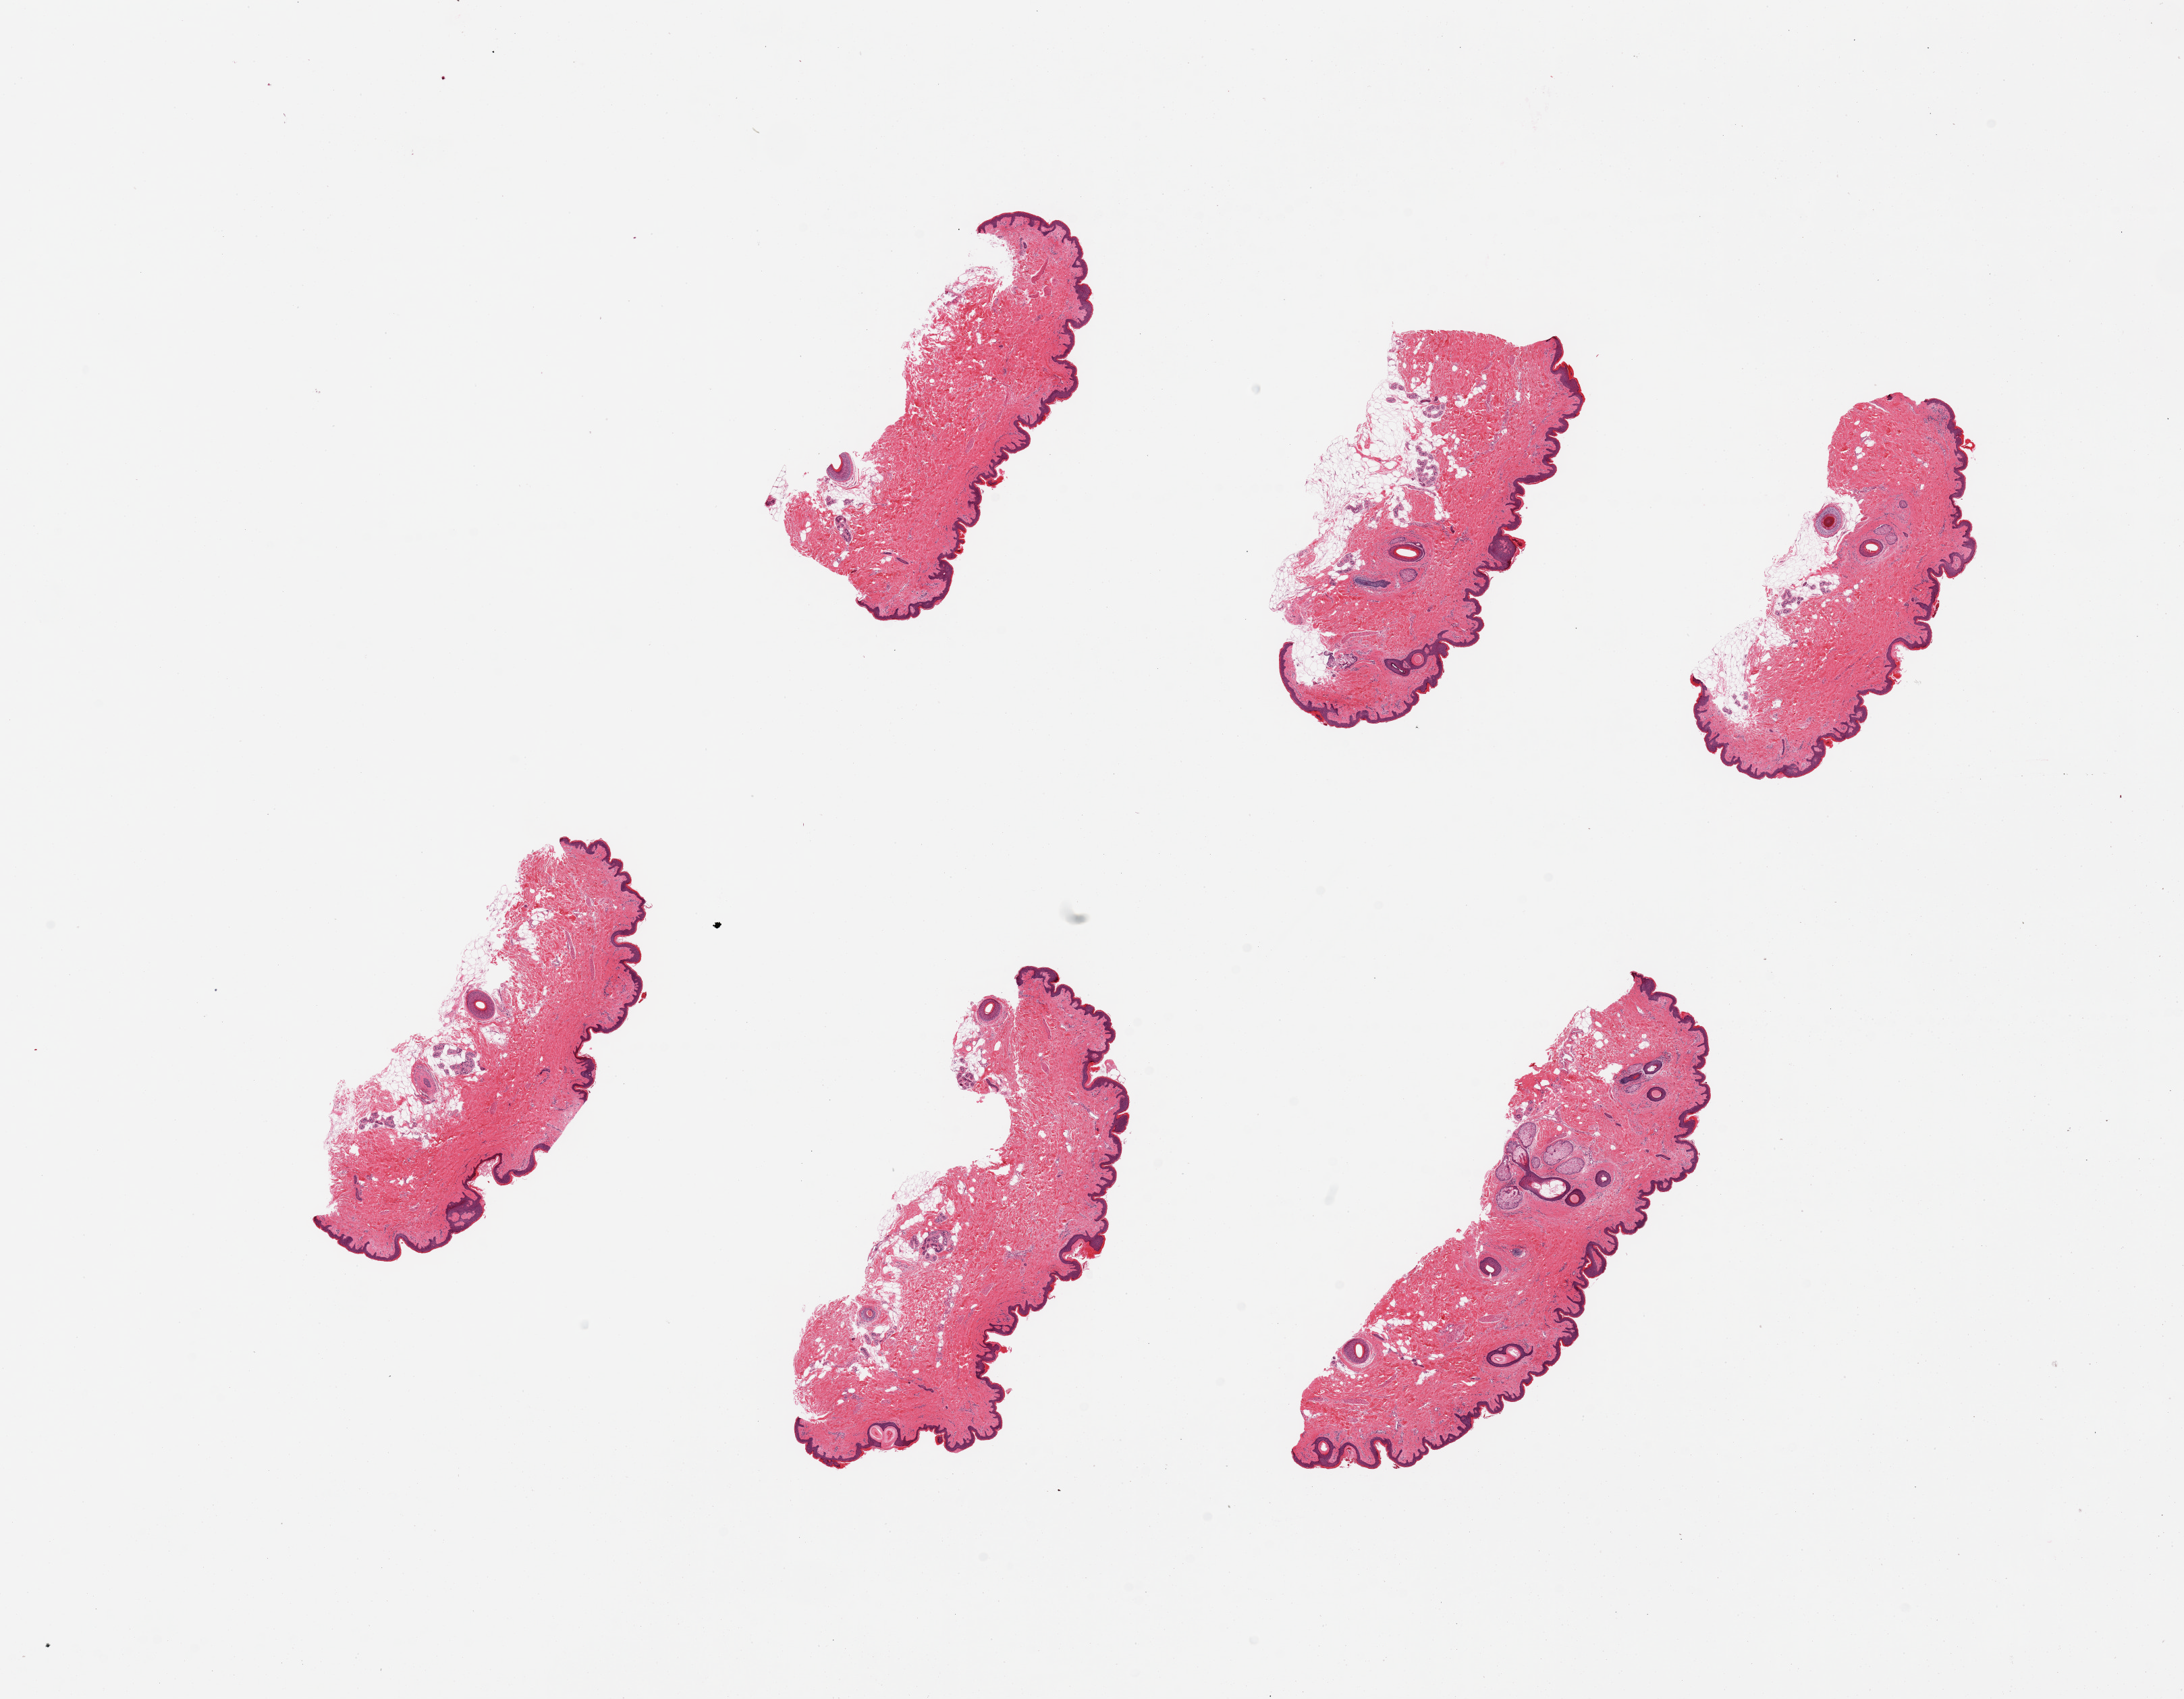
Whole-slide image, hematoxylin and eosin (H&E) stain, brightfield — a low-resolution overview of the entire scanned area, about 25.6 x 19.9 mm; PAXgene-fixed, paraffin-embedded tissue; section of skin of suprapubic region (target tissue); tissue donor sample. Donor sex: female.
Reviewer comment on this tissue sample: 6 pieces focal adherent fat on a few.